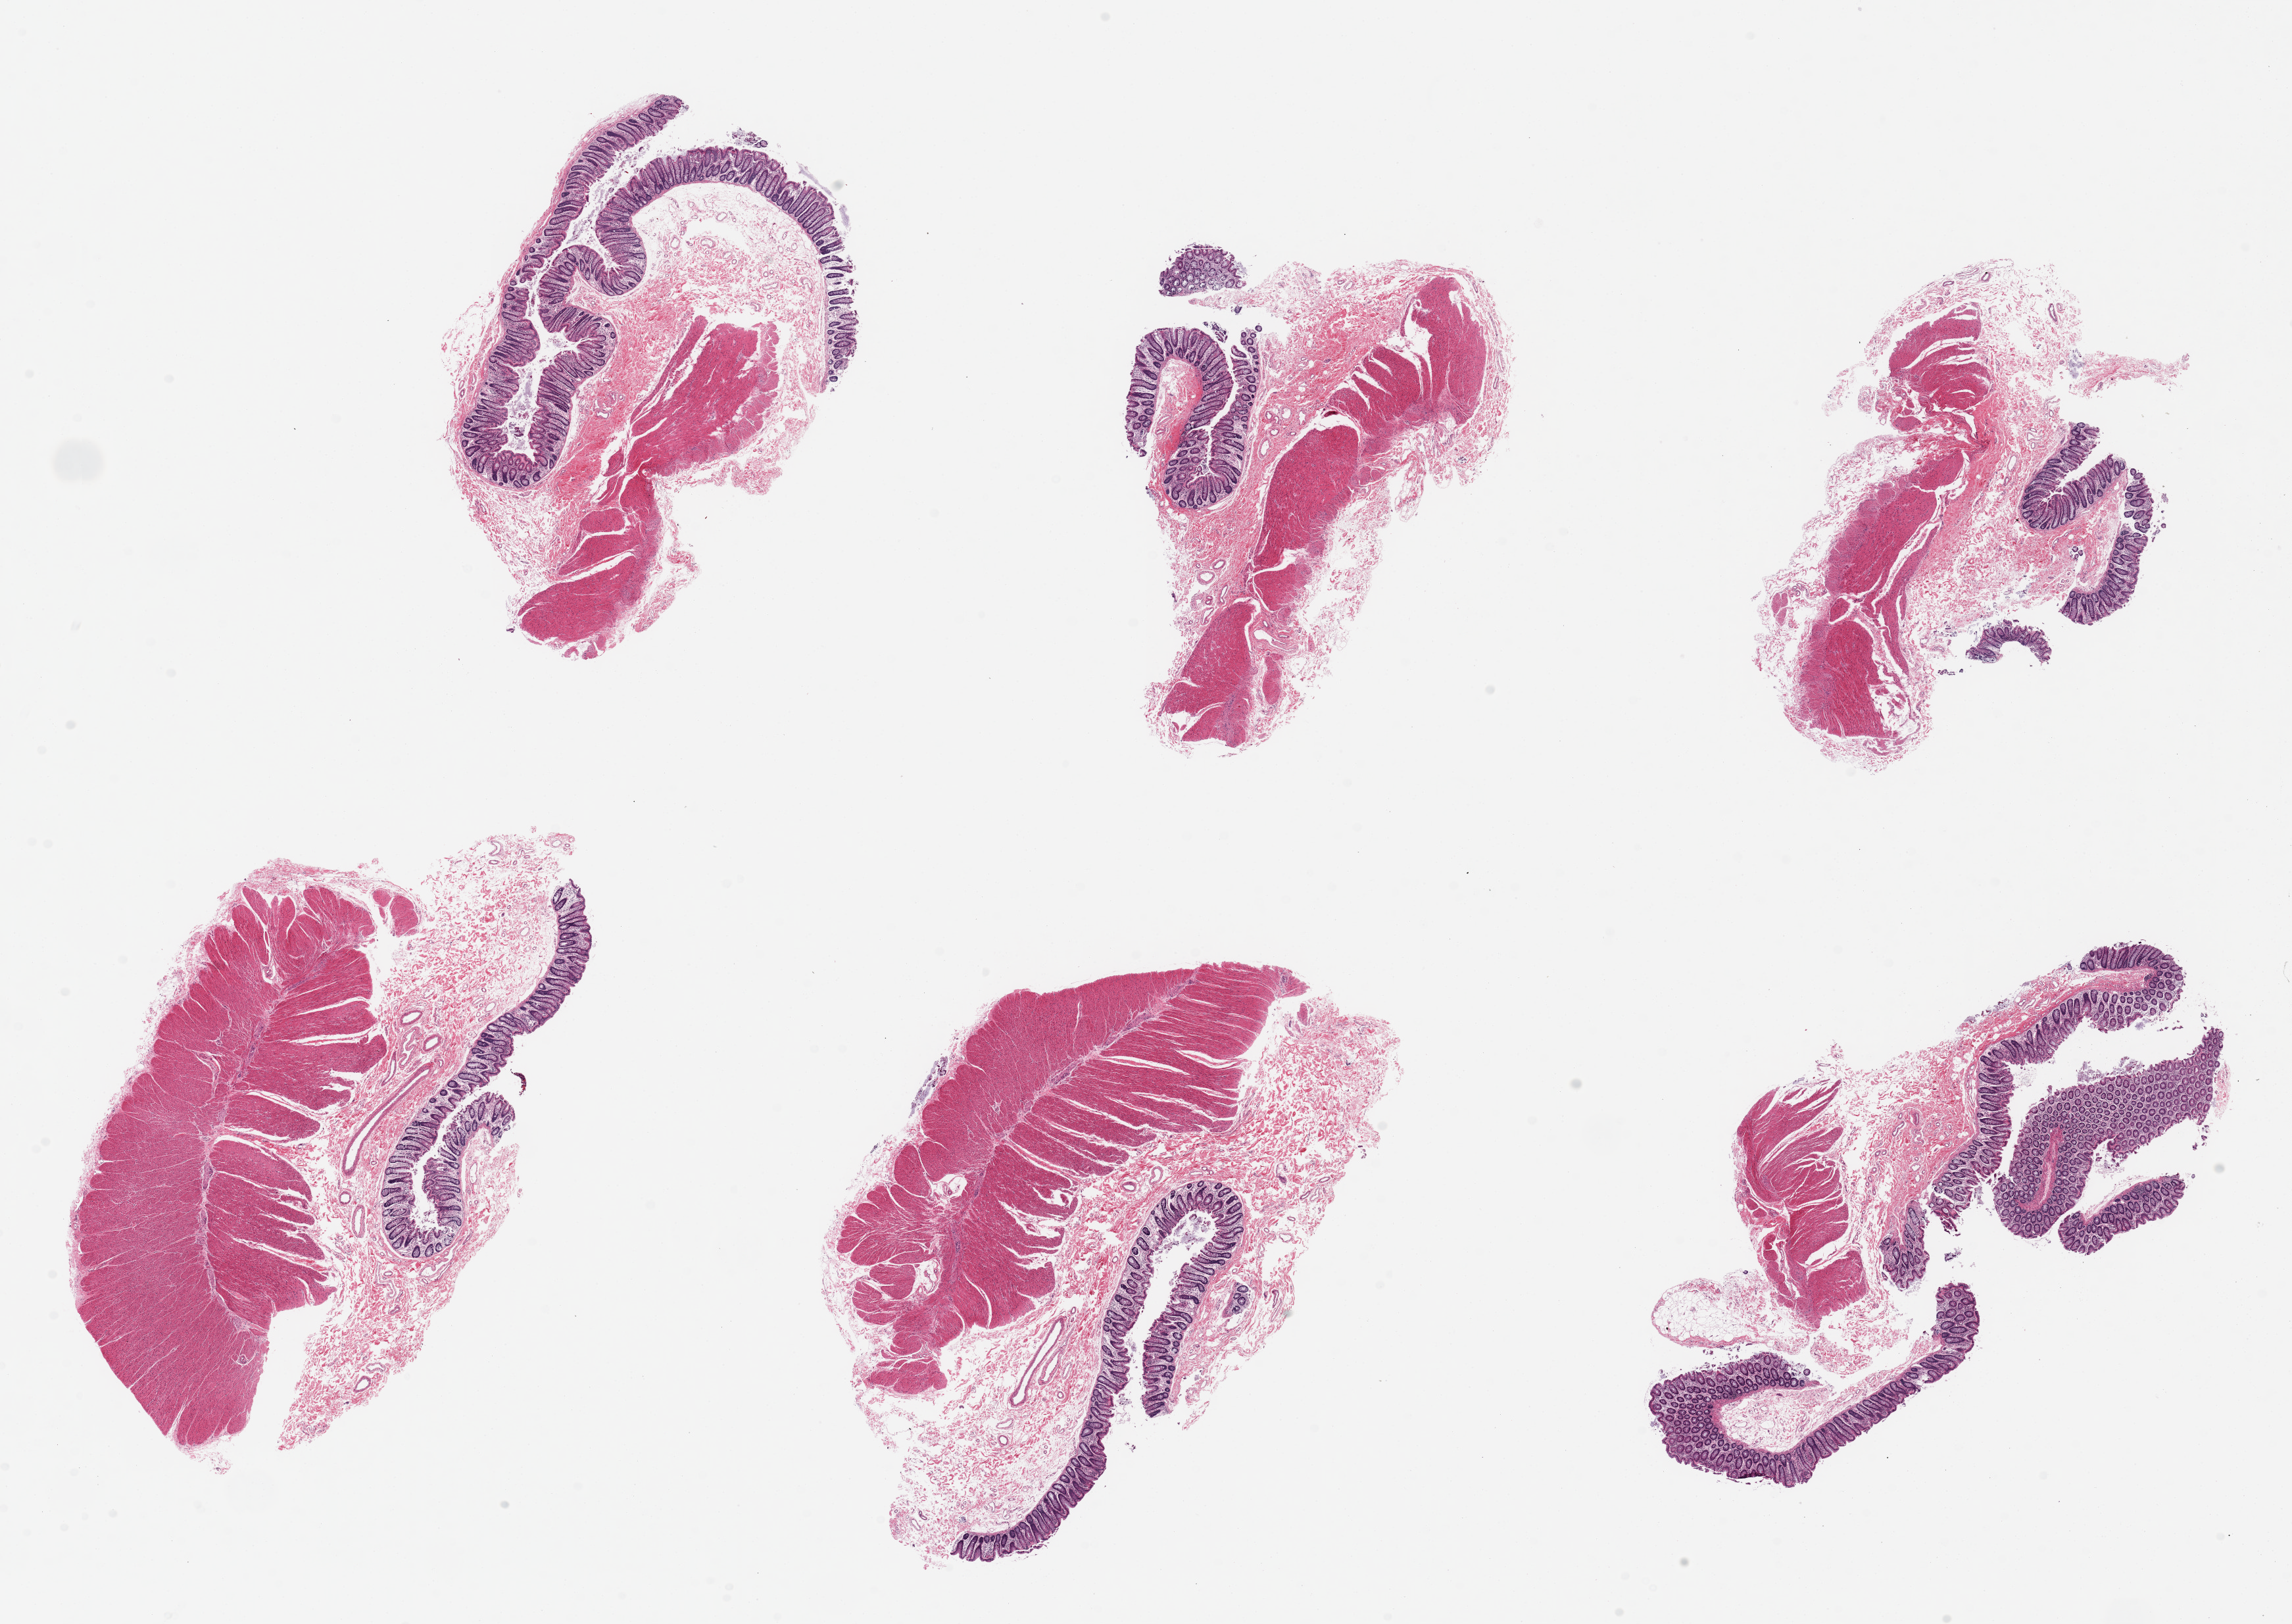
Whole-slide image, haematoxylin and eosin stain — low-resolution overview of the scanned area, about 27.6 x 19.5 mm; PAXgene-fixed, paraffin-embedded tissue; target tissue: transverse colon; donor tissue sample. Donor sex: male.
Pathologist's review note for this sample: ~6x3mm 6 pieces ~10% mucosa, moderately well preserved.